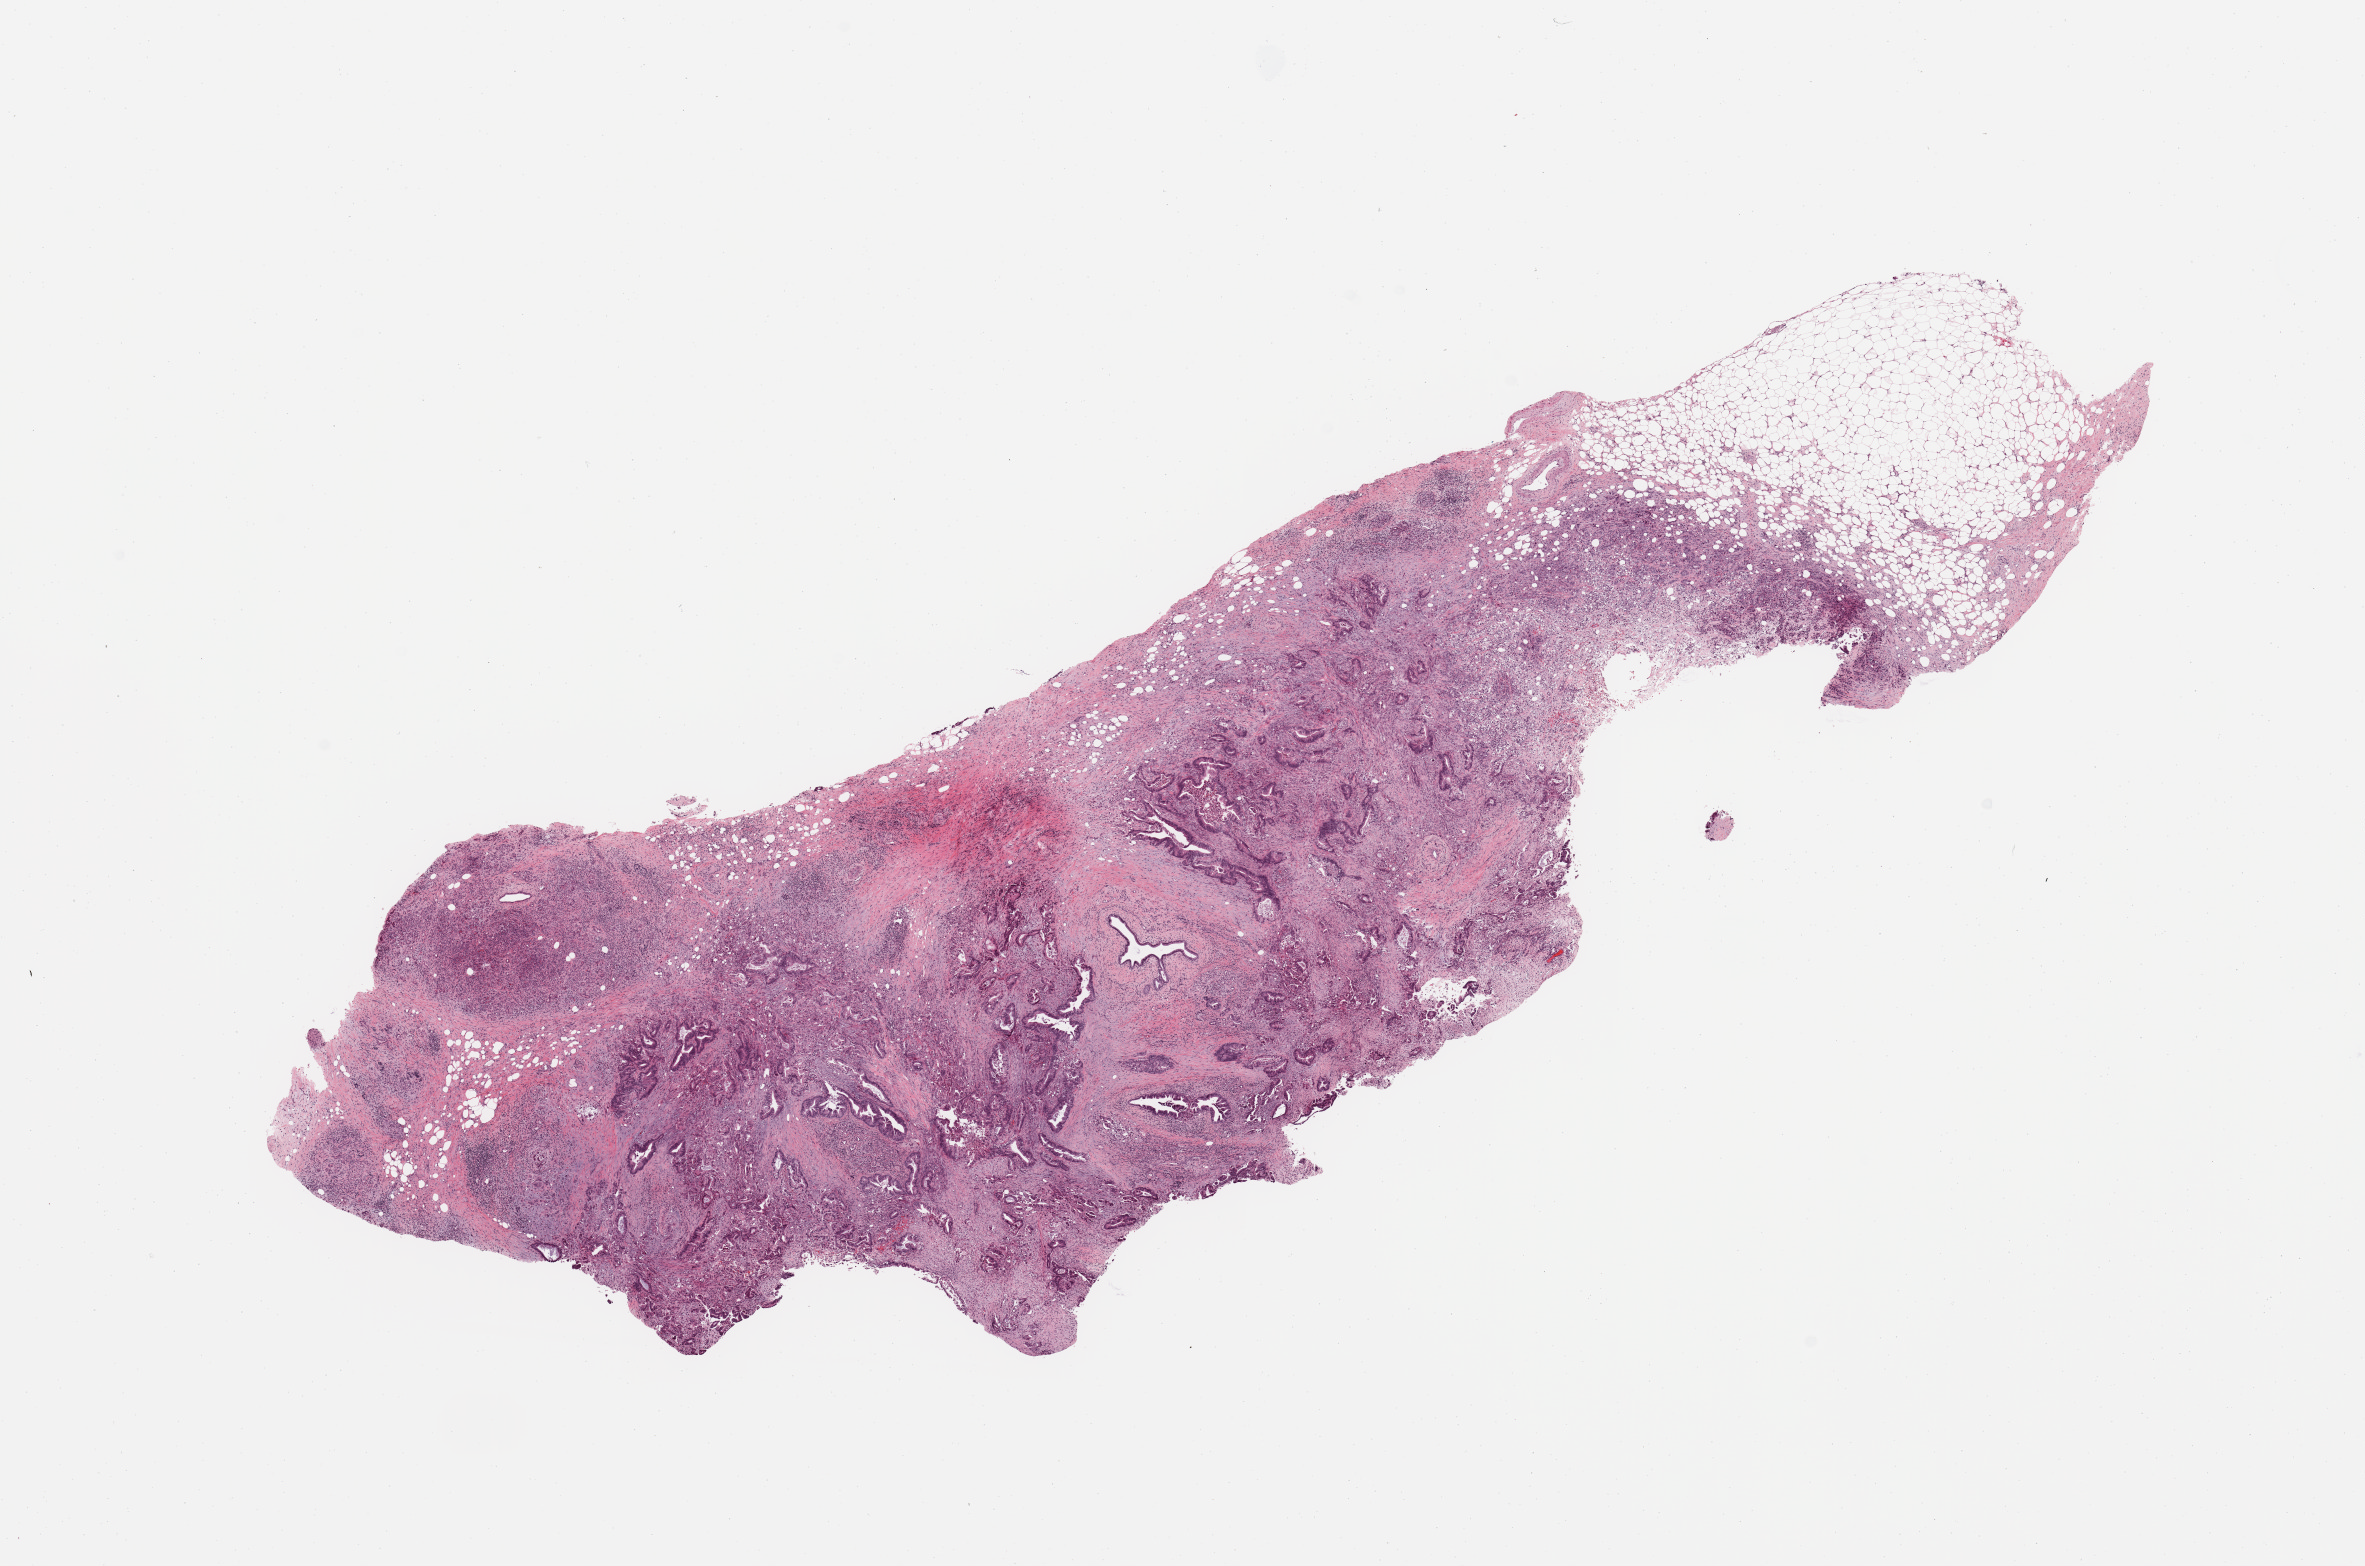
Hematoxylin and eosin (H&E) stained whole-slide image — a low-resolution overview of the entire scanned area, about 18.7 x 12.4 mm (slide scanned at 20x). Tumour tissue sample, sampled site: pancreas. Male, 74 y/o. Histologic grade: G3 (poorly differentiated). Composition of this section per pathologist review: tumour nuclei 60%, necrosis 0%.
AJCC pathologic stage: IIB. Primary tumour site (as recorded): head. Histologic diagnosis: Infiltrating duct carcinoma, NOS.